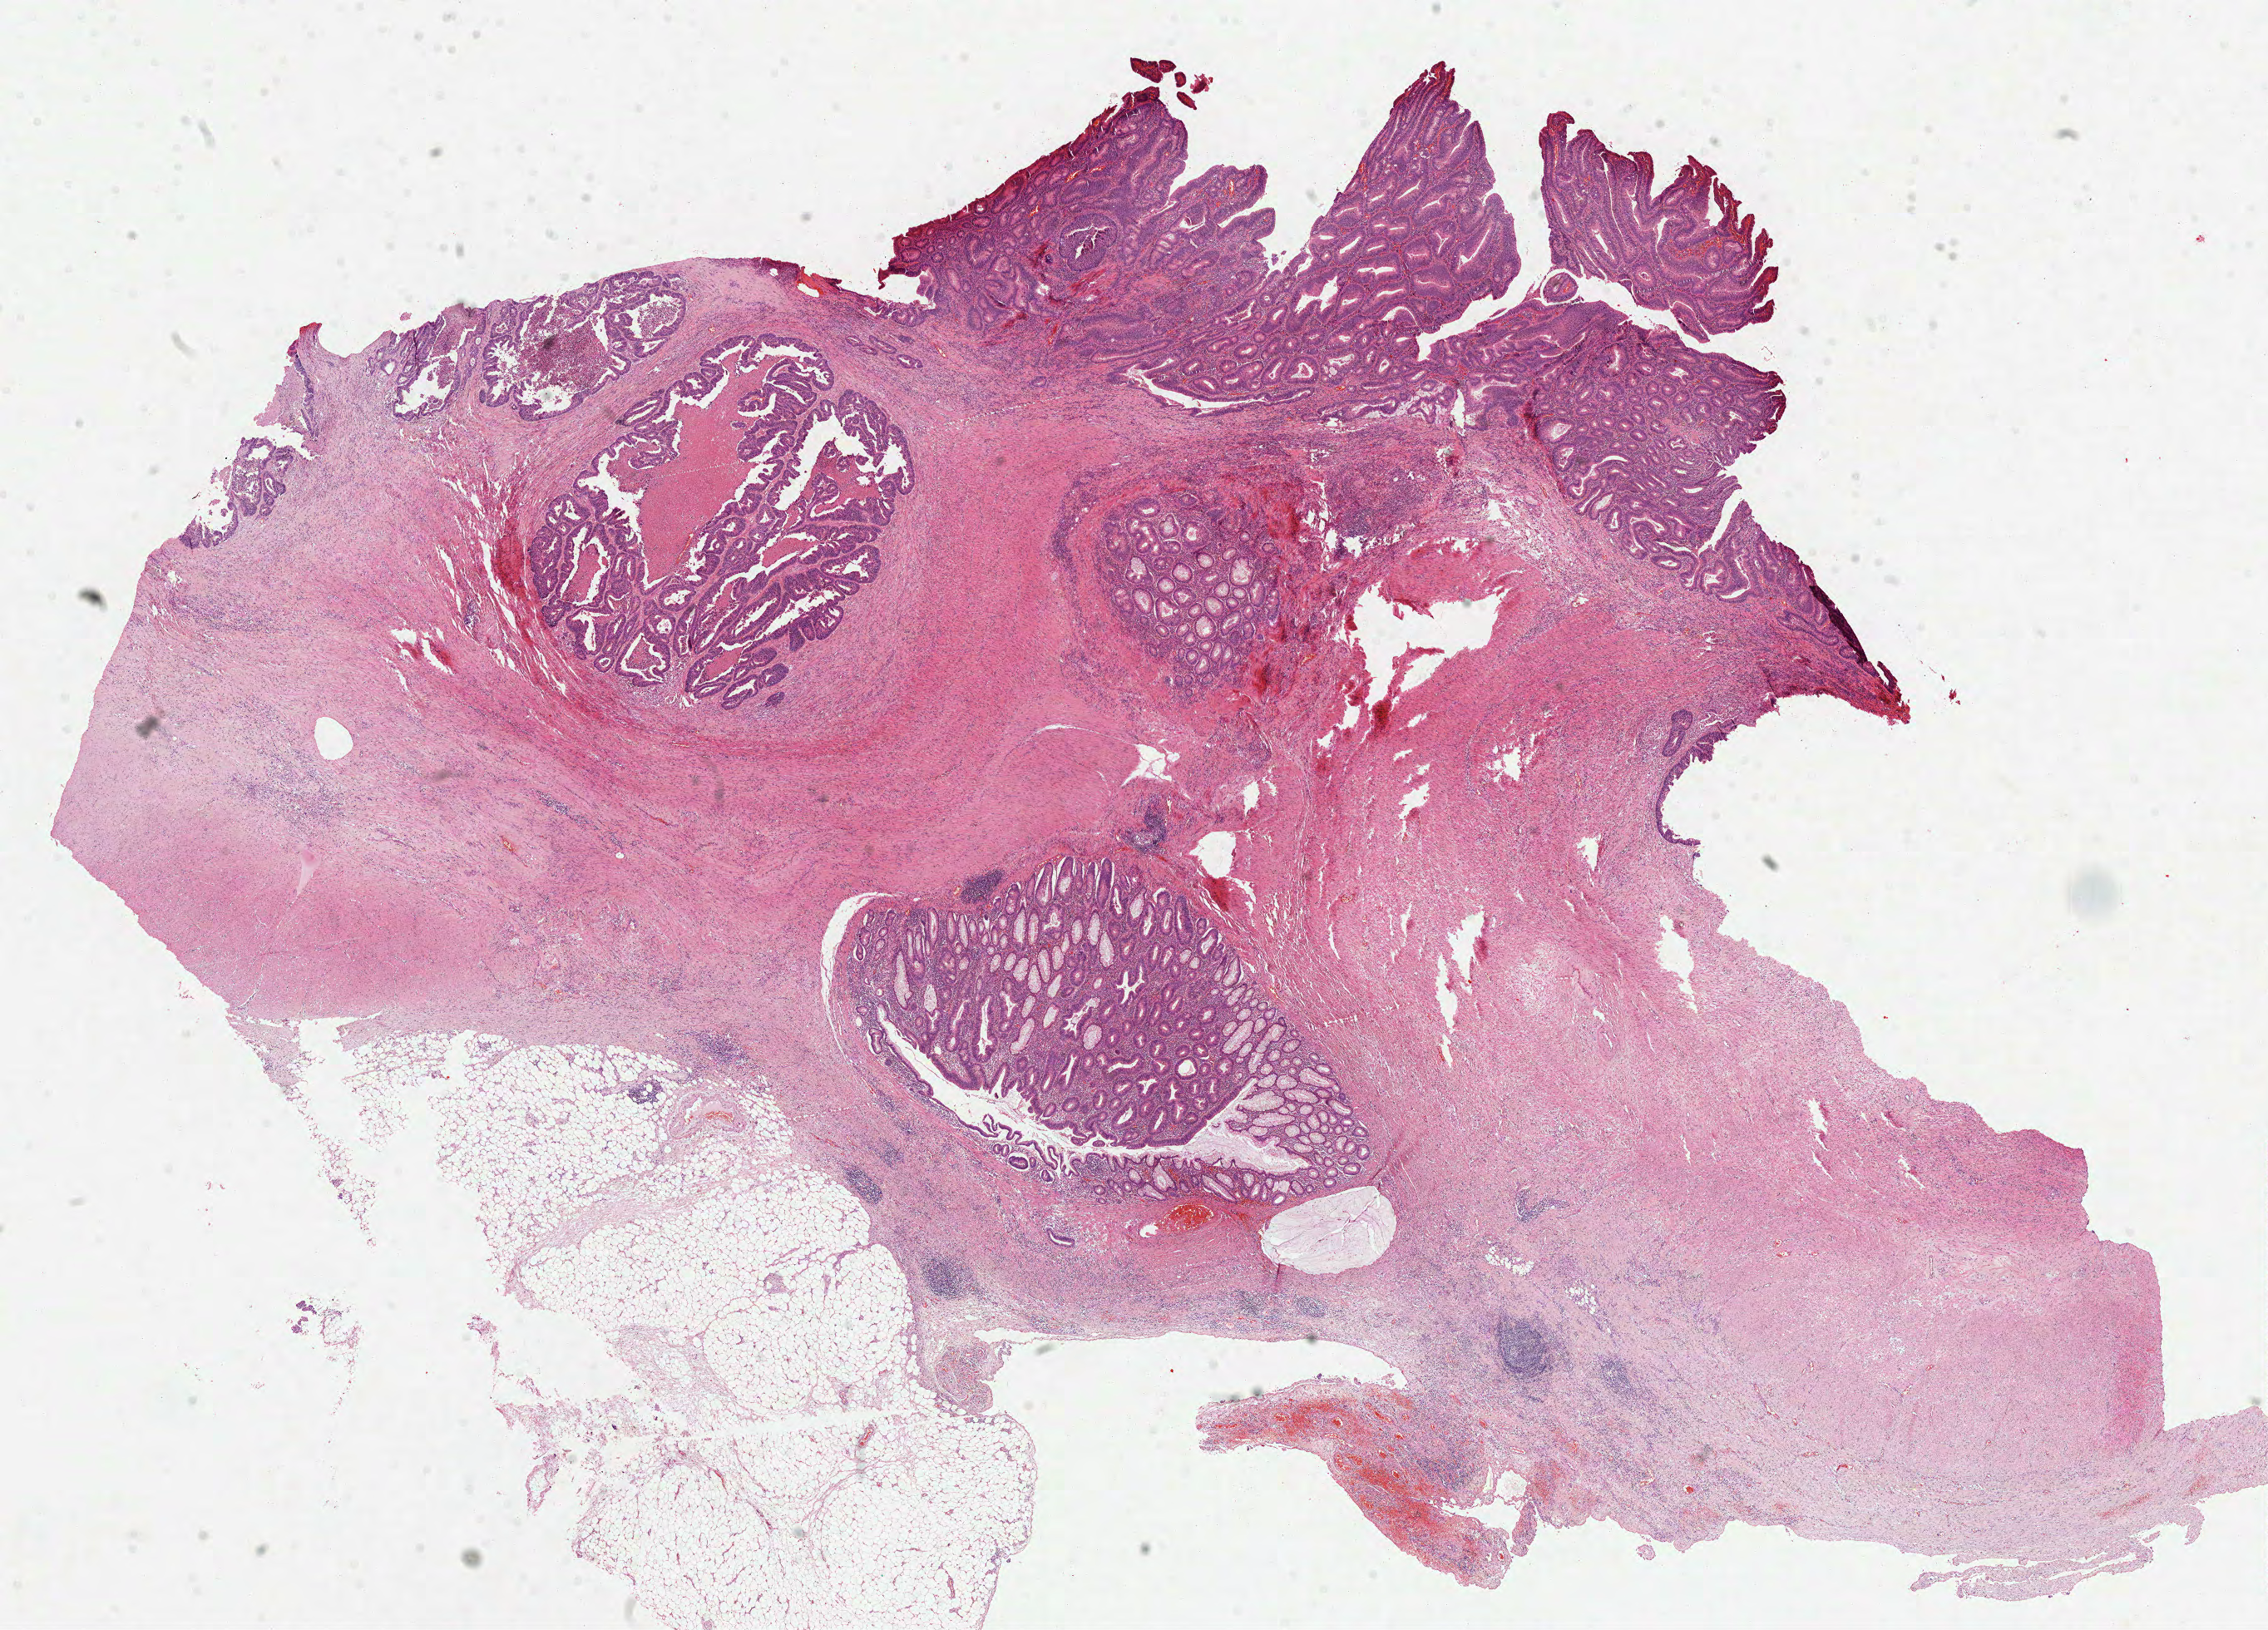
Whole-slide histology image, H&E-stained, a low-resolution overview of the entire scanned area, about 22.0 x 15.8 mm. FFPE section. Rectum, primary tumour sample. Female patient; age at initial diagnosis 77 years.
Lymph nodes positive (case pathology): 0 of 3 examined. Histologic diagnosis: Adenocarcinoma in tubulovillous adenoma.